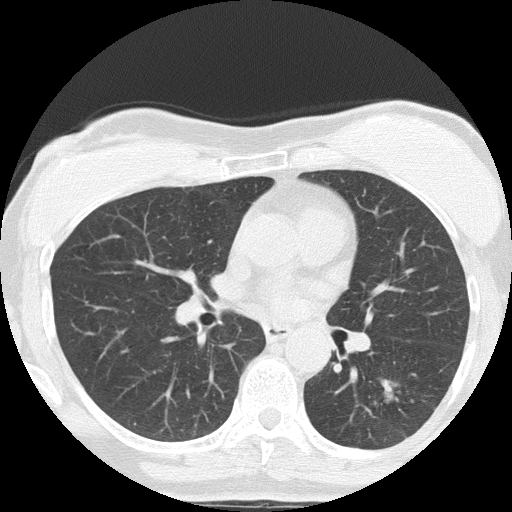
Chest CT (low-dose screening protocol), one axial image; third annual screen; lung window (W 1500 / L -600 HU); lung (sharp) reconstruction kernel (FC51); slice 72 of 152 in the series. Female, age 64 years at enrolment. Former smoker at enrolment.
Expert reader's lesion annotation, bounding box (x1, y1, x2, y2) in pixels: (369, 361, 460, 439). The screening reader recorded 3 non-calcified nodules or masses ≥4 mm on this exam (right upper lobe, left lower lobe, right middle lobe); which of them this box marks is not recorded. Lung cancer was diagnosed 212 days after this screen: adenocarcinoma, NOS, left lower lobe, moderately differentiated (G2), stage IA (AJCC 6th edition), 17 mm at pathology.